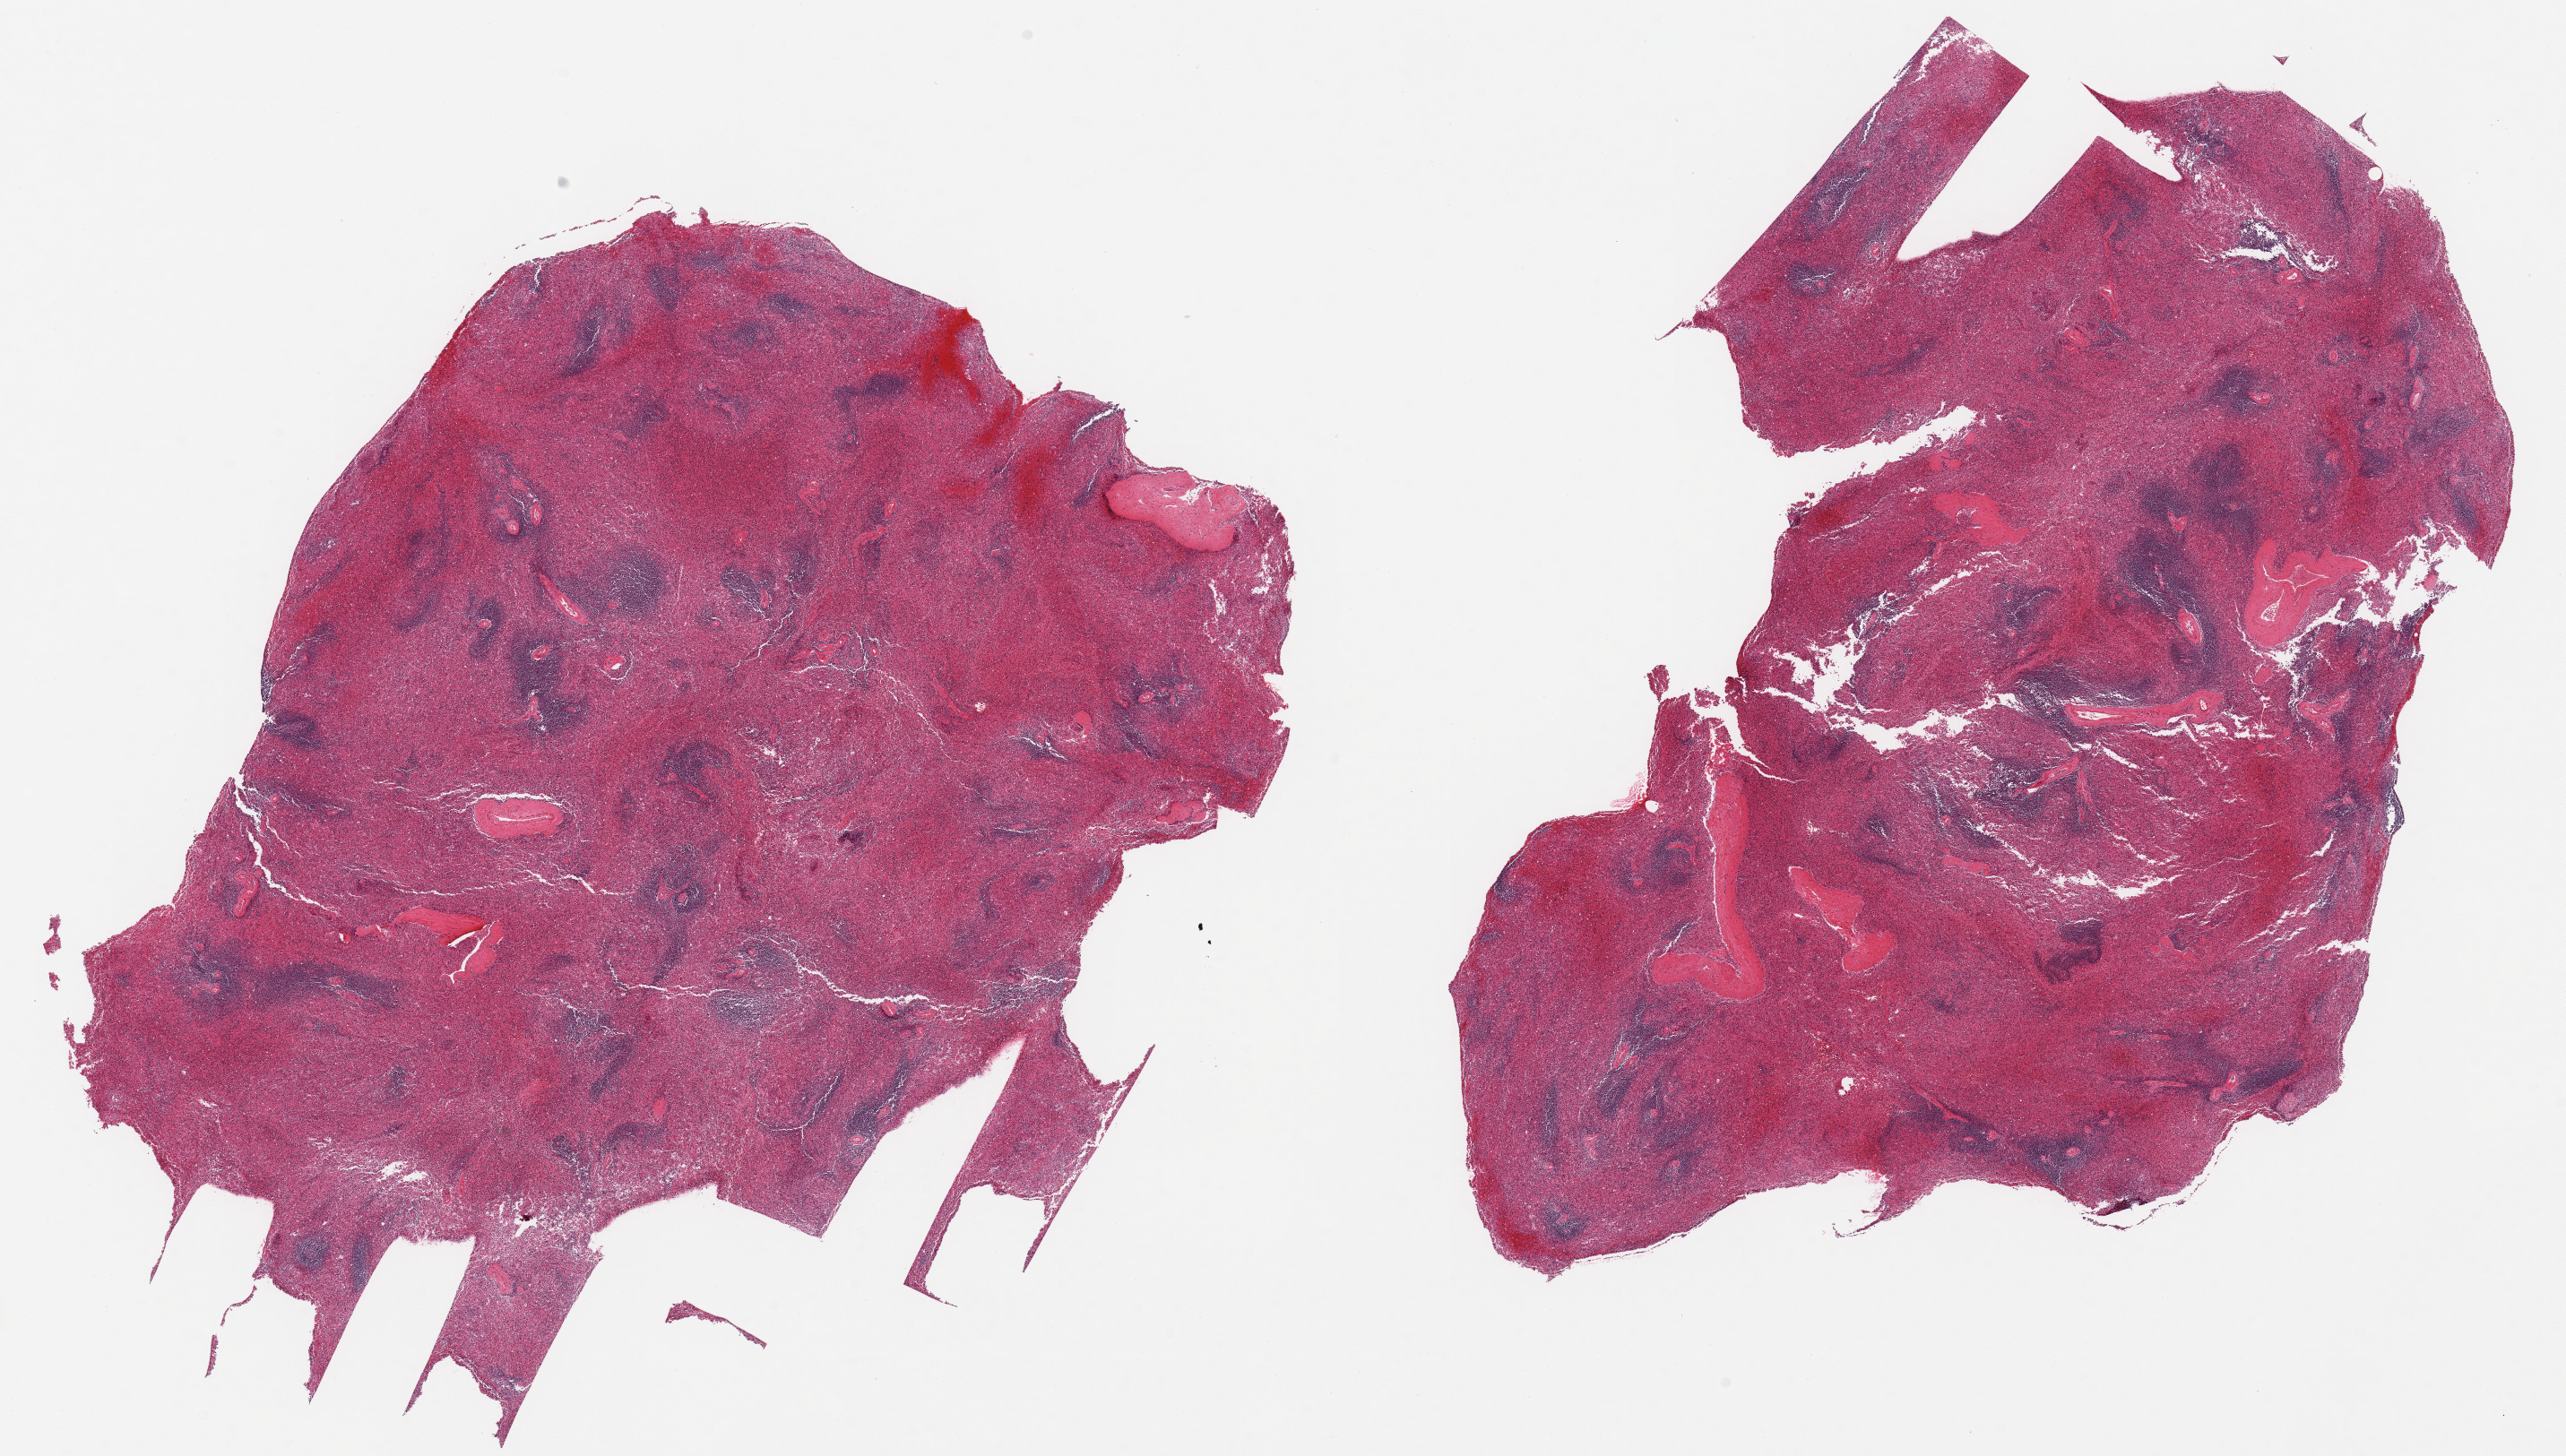
Haematoxylin and eosin whole-slide image — a low-resolution overview of the entire scanned area, about 22.6 x 12.9 mm (acquisition: 20x scan); PAXgene-fixed, paraffin-embedded tissue; section of spleen (target tissue); tissue donor sample.
Reviewer comment on this tissue sample: 2 pieces, moderate congestion.